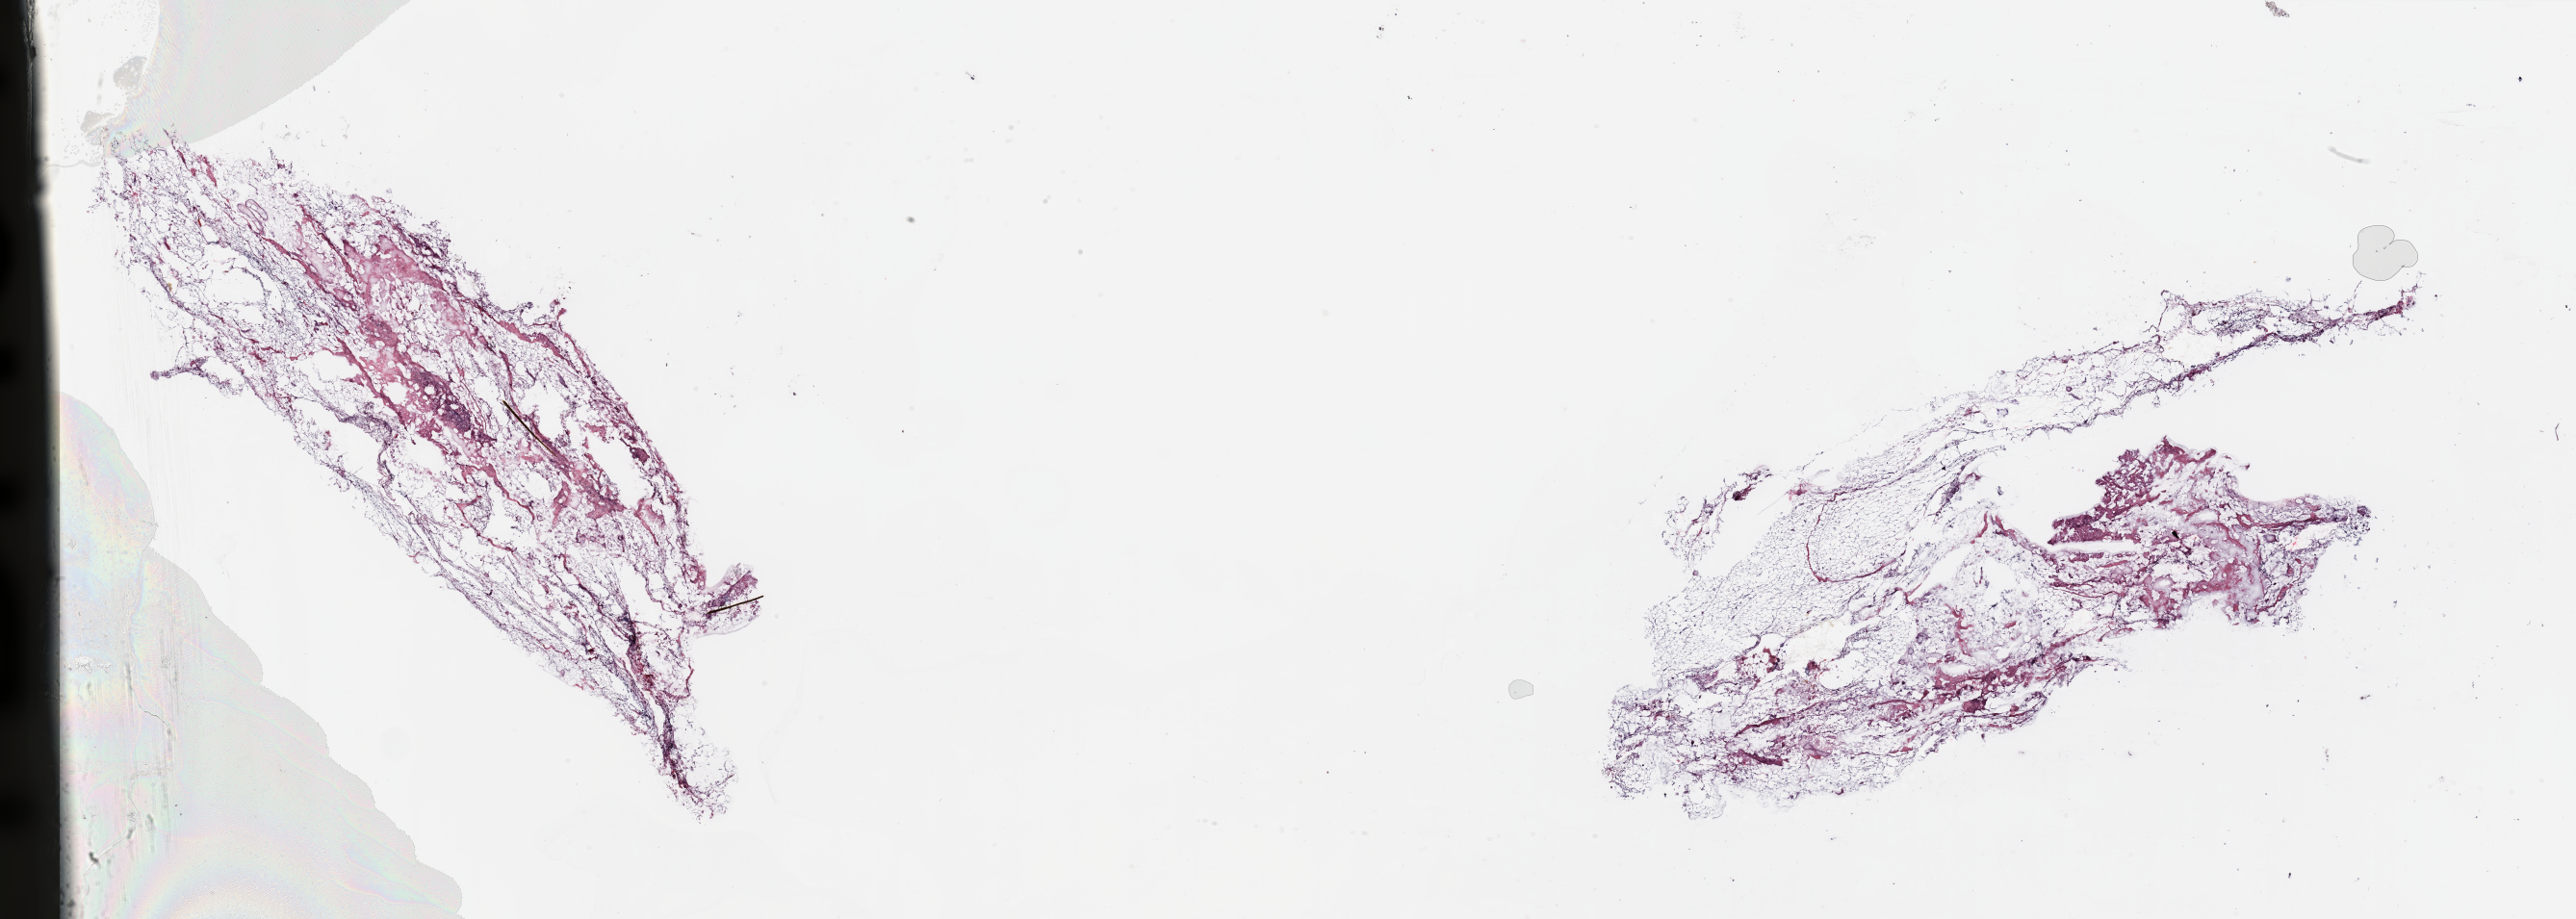
Whole-slide histology image, H&E, low-resolution overview of the scanned area, about 42.3 x 15.1 mm (from a 20x scan). Tumour tissue sample, breast. 74-year-old female patient.
Diagnosis: Infiltrating duct carcinoma, NOS. AJCC pathologic stage: IIIA.